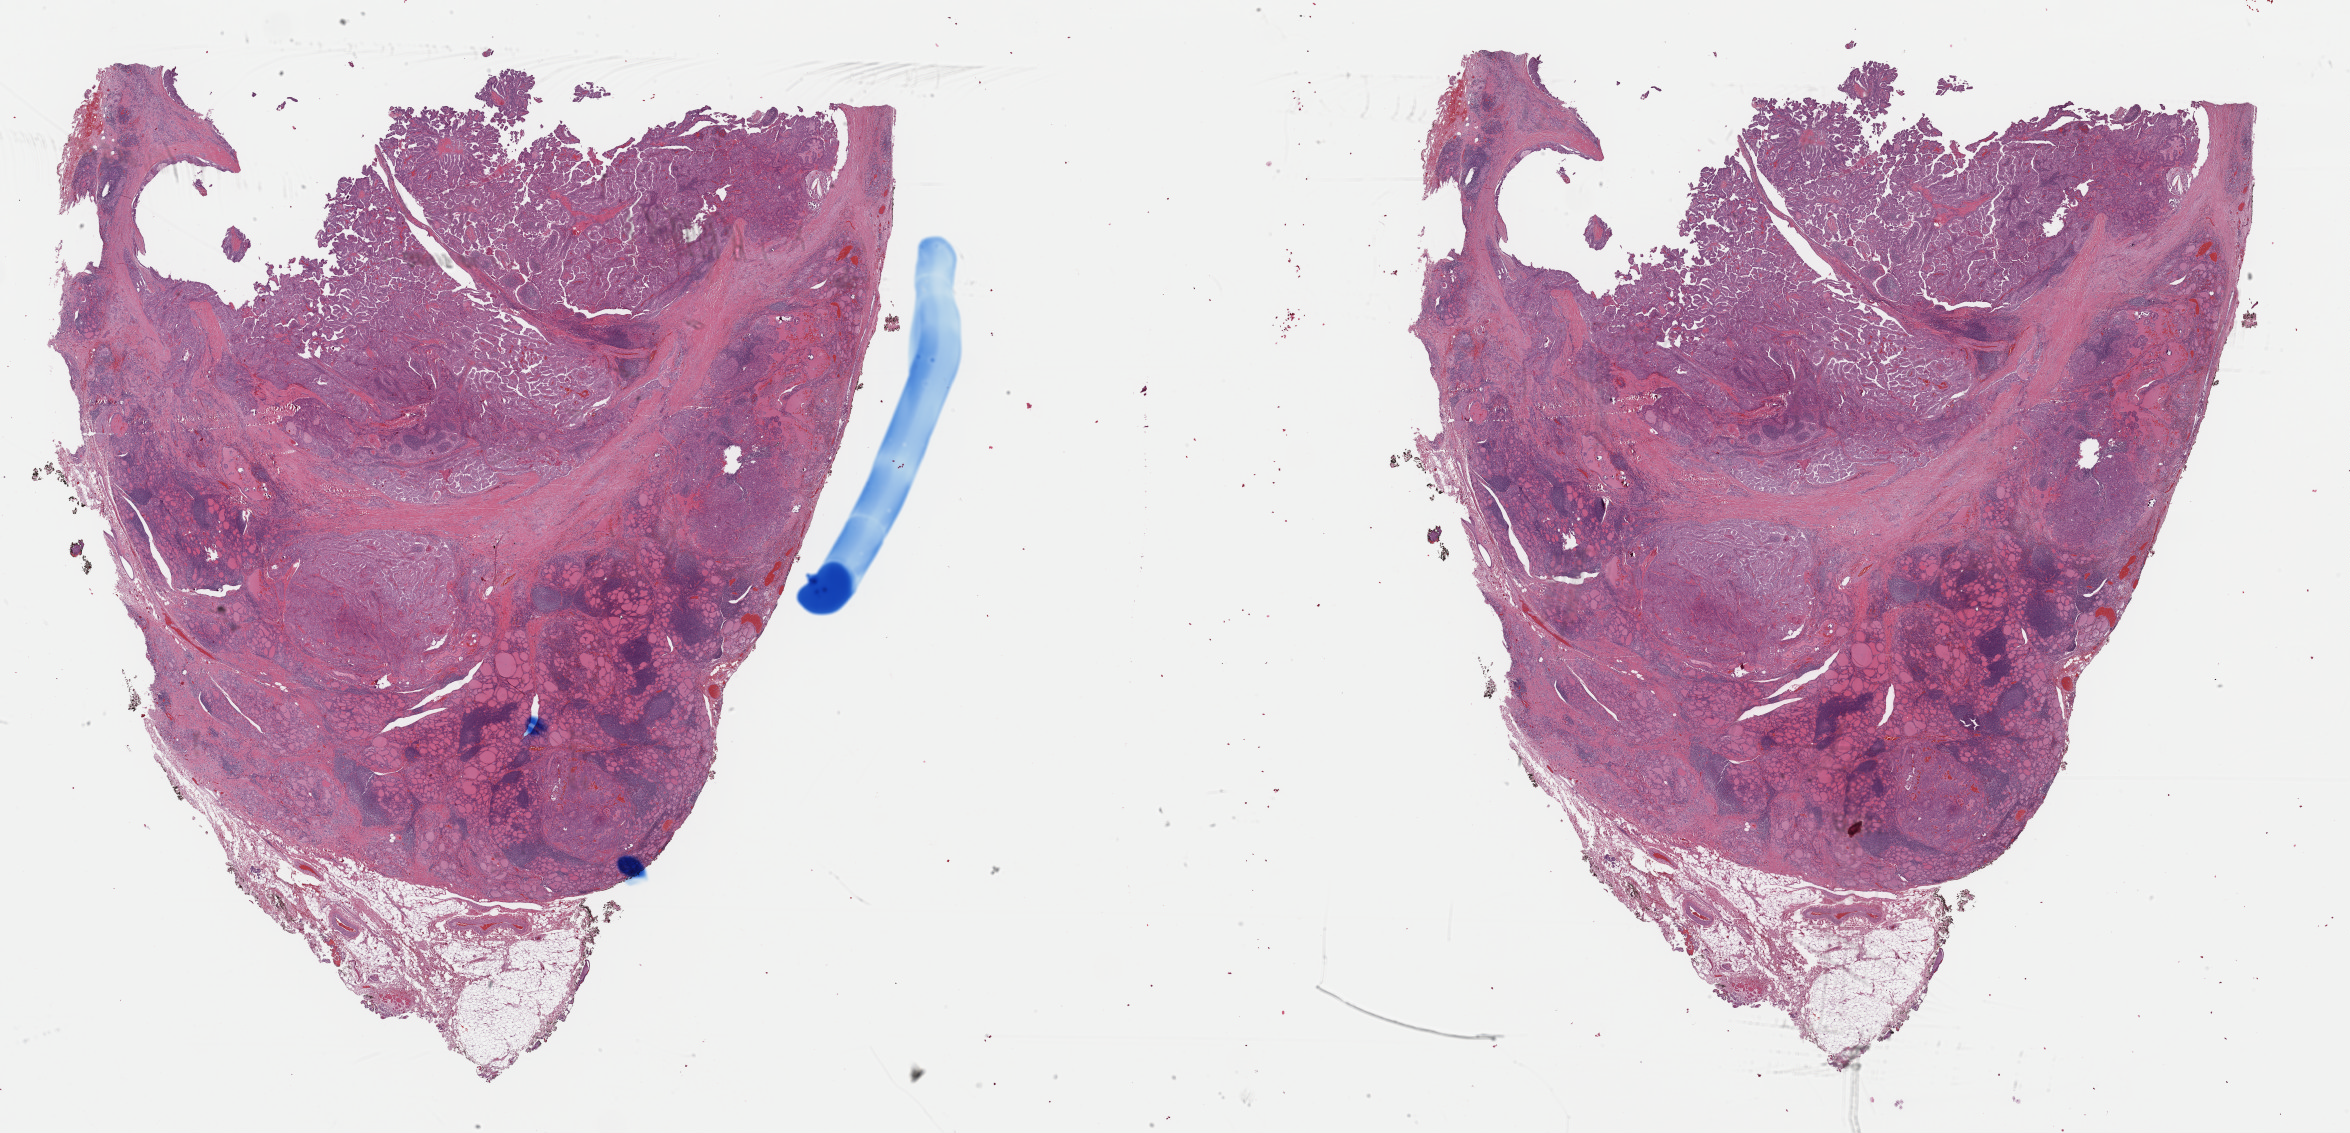
Digitized H&E-stained tissue section (whole slide), shown as a low-resolution overview of the whole scanned area (about 37.1 x 17.9 mm). Formalin-fixed paraffin-embedded (FFPE) diagnostic section. Thyroid, primary tumour sample. Patient: male, age at initial diagnosis 37 years.
Laterality: right. Histologic diagnosis: Nonencapsulated sclerosing carcinoma (thyroid gland). Lymph nodes positive (case pathology): 9 of 11 examined. AJCC pathologic stage: I.